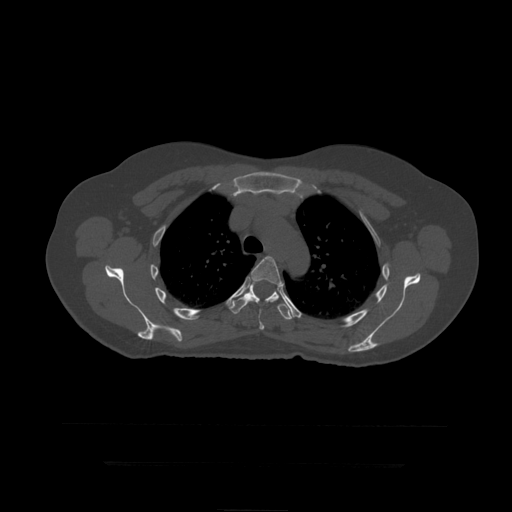
CT including the spine, one axial slice. Position 328 of 399 along the scan axis. Bone window (W 1800 / L 400 HU). 512 × 512 image matrix, field of view 450 × 450 mm. Patient age 41 years. Case-level facts recorded for this patient, not image findings: primary cancer: breast.
Structures marked on this image (semi-automatically segmented with operator editing):
- T5 vertebra: bounding box [x1, y1, x2, y2] px = [242, 256, 281, 330]
- T6 vertebra: [227, 282, 295, 320]